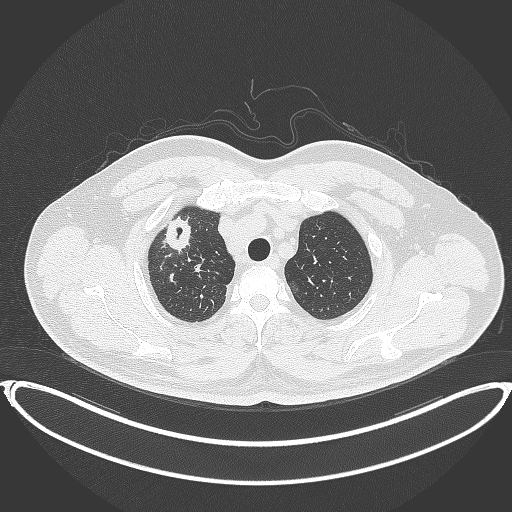
Chest CT, one axial slice. Slice 330 of 399 in the series (ordered by position). Lung window (W 1500 / L -600 HU). 1 mm slice thickness. 512 × 512 image matrix. Male patient, age 53 years. Case-level facts recorded for this patient, not image findings: clinical TNM (as recorded): T2a N0 M0.
Annotated regions visible in this slice (rectangle marked by the reading radiologist):
- lung tumour (recorded histology: adenocarcinoma): bounding box <163,213,198,255> (left, top, right, bottom; pixels)